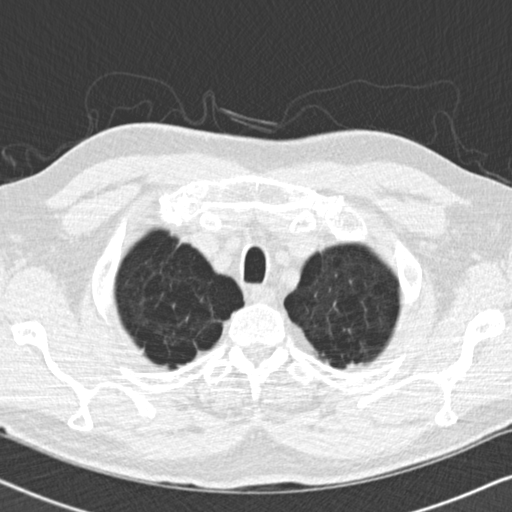
Low-dose screening chest CT, one axial slice; slice 159 of 175 in the series (ordered by position); reconstruction kernel B30f; 120 kVp; lung window (W 1500 / L -600 HU); 2 mm slice thickness; 512 × 512 image matrix, field of view 330 × 330 mm.
Annotated regions visible in this slice (expert manual segmentation):
- lesion 1 (tumor, upper lobe of left lung): box from (x=346, y=362) to (x=367, y=370) px